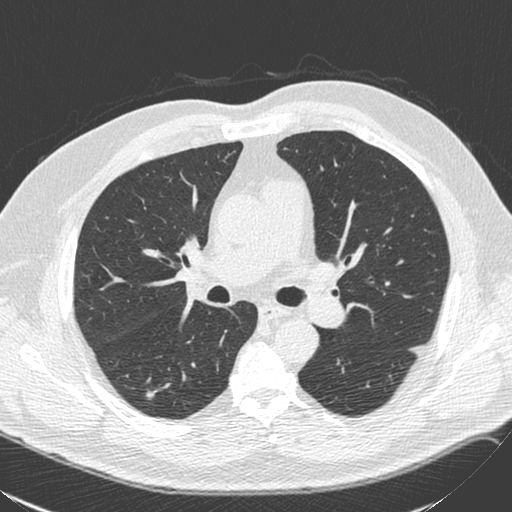
Axial slice from a low-dose chest CT screening exam; baseline annual screen; lung window (W 1500 / L -600 HU); 1.3 mm slice thickness; standard (soft-tissue) reconstruction kernel (C); slice 94 of 248 in the series. Male participant, aged 71 years at enrolment. Former smoker at enrolment.
Expert-annotated lung lesion, bounding box [x1, y1, x2, y2] px = [140, 381, 173, 409]. The exam's reader record, not a measurement of the box and not confirmed to be the same lesion: non-calcified nodule or mass ≥4 mm, right lower lobe, 6 × 6 mm, smooth margins, soft tissue attenuation. Lung cancer was diagnosed 231 days after this screen: squamous cell carcinoma, NOS, right lower lobe, poorly differentiated (G3), stage IA (AJCC 6th edition), 4 mm at pathology.